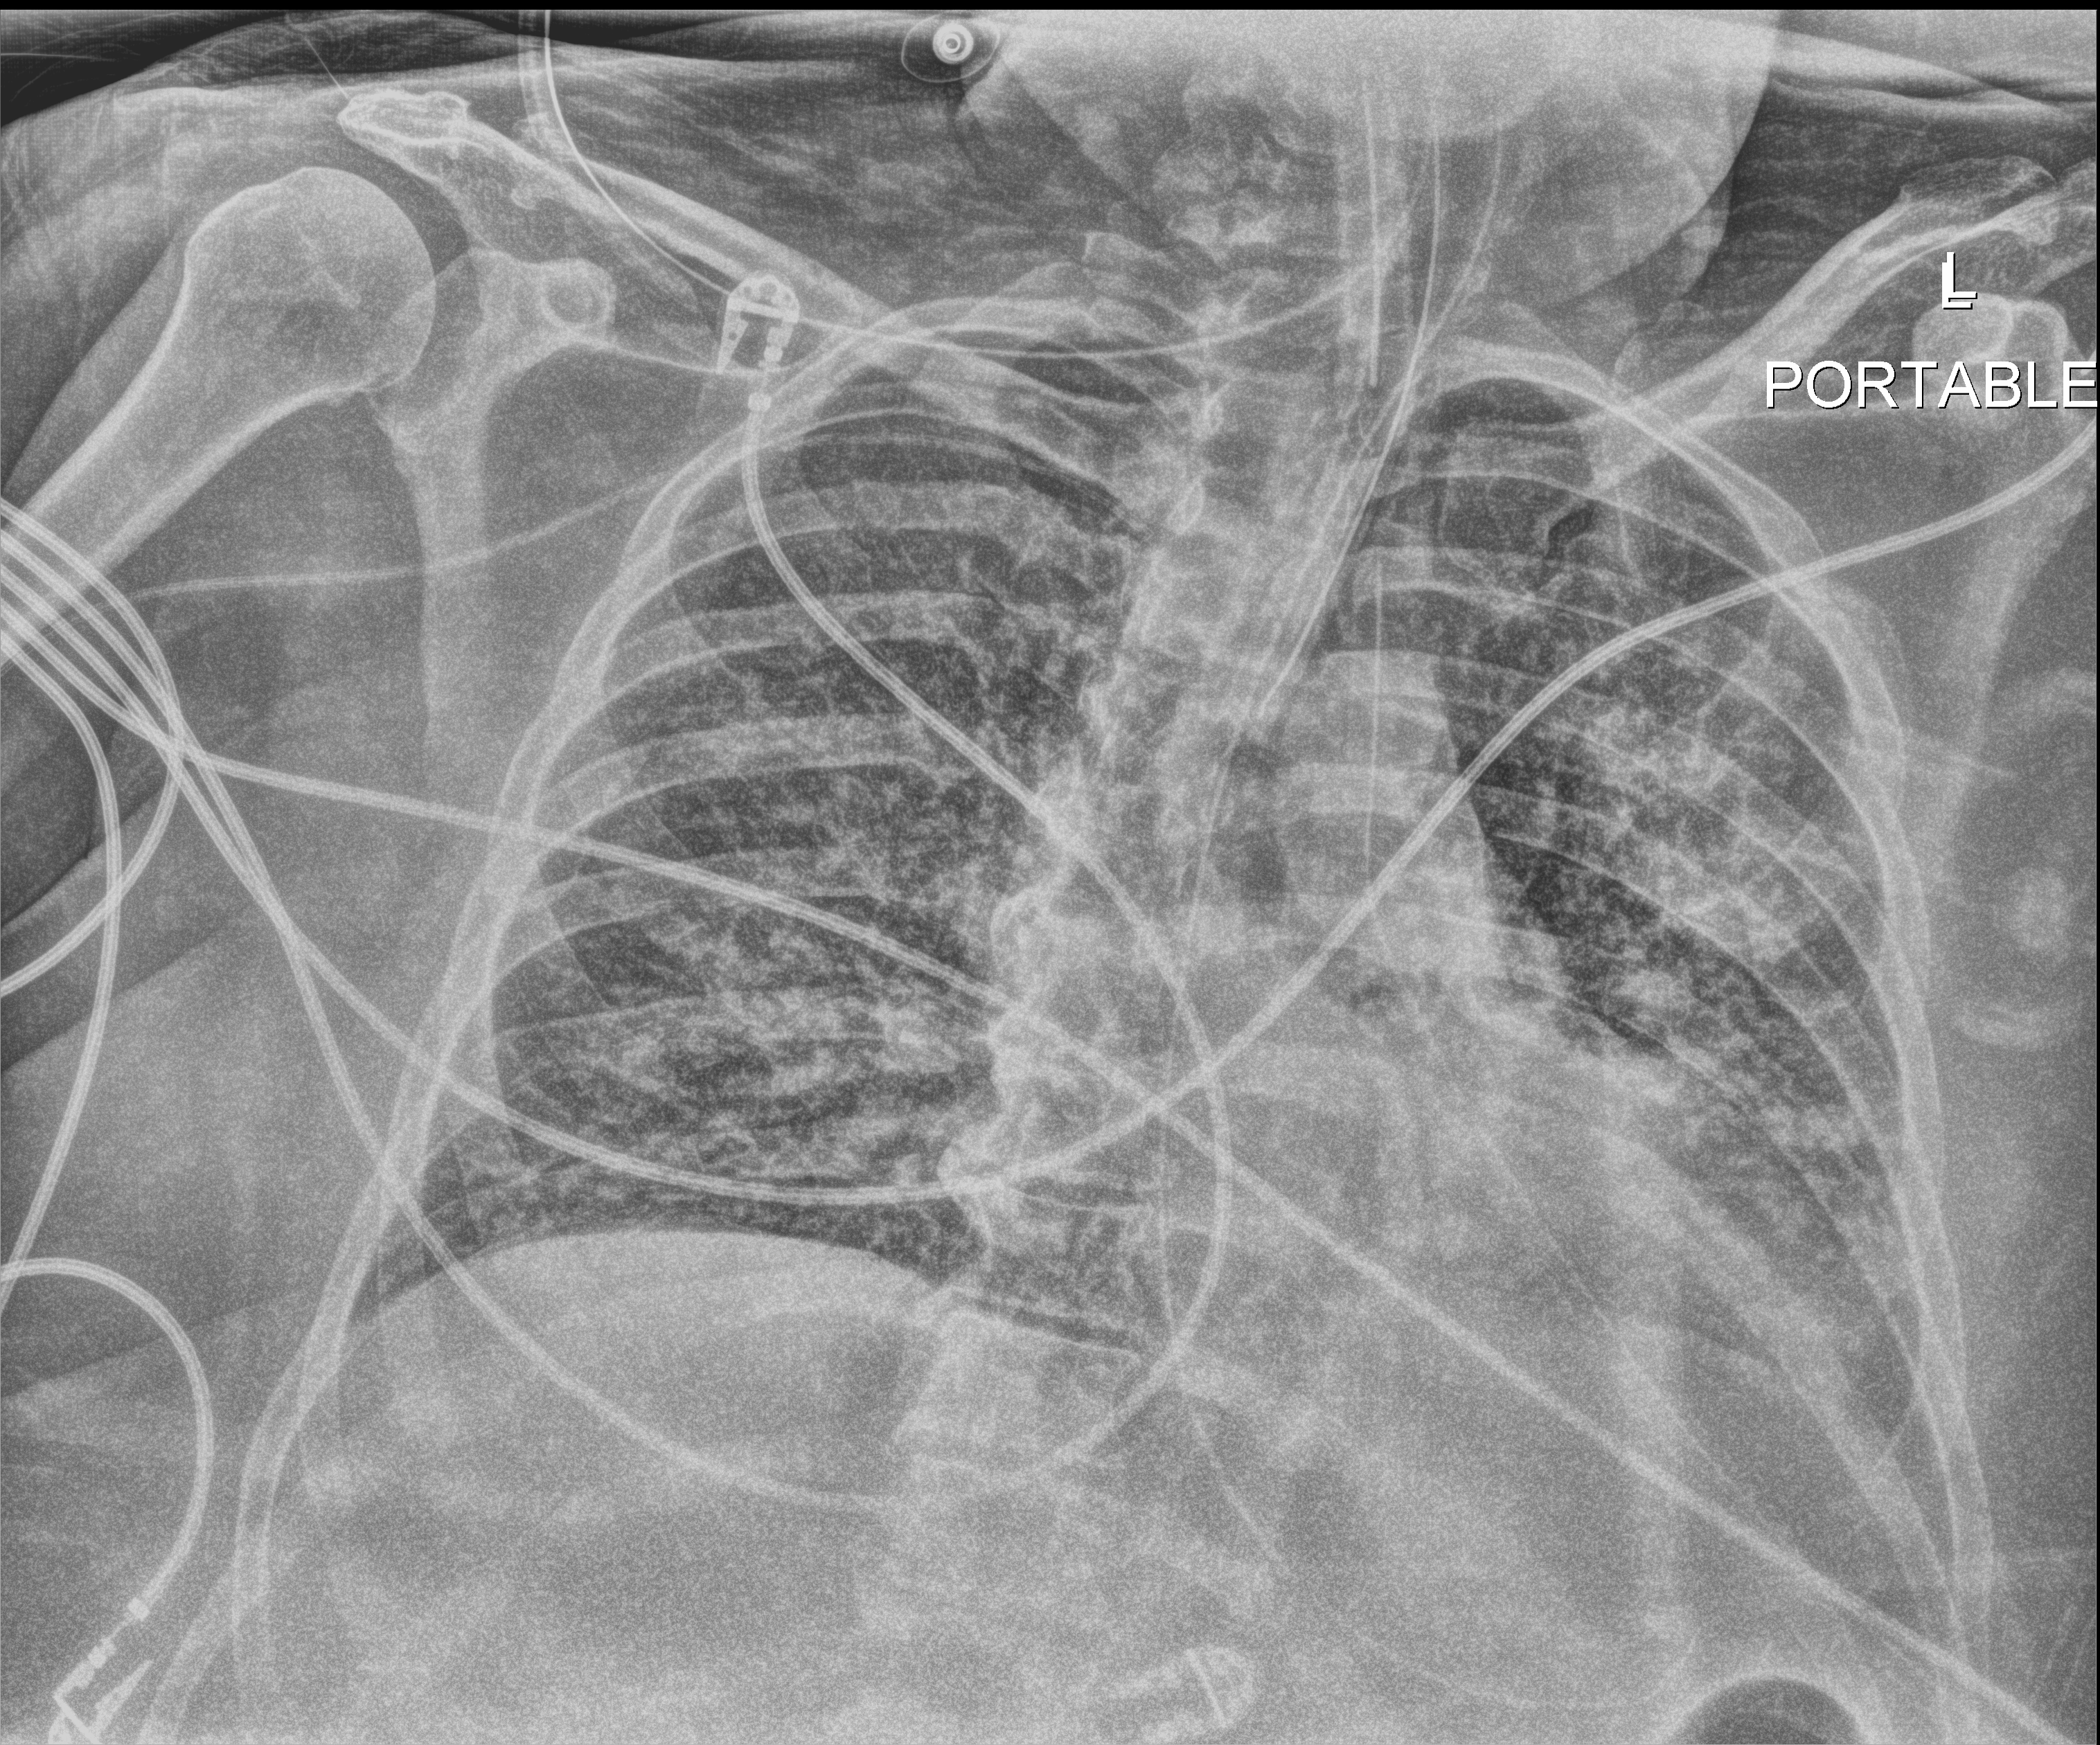
Chest X-ray; anteroposterior (AP) projection. Patient hospitalised with COVID-19, aged 18–59 years.
Hospital-stay facts (about this admission, not read from this image; timing relative to this image not recorded):
- mechanically ventilated during this hospital stay: yes
- admitted to intensive care during this hospital stay: yes